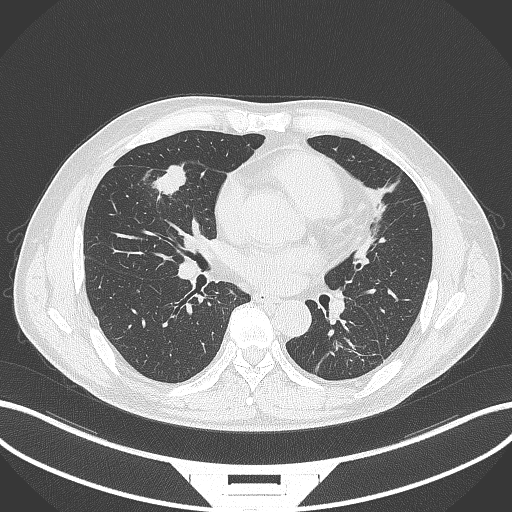
Chest CT, one axial slice. Slice 146 of 399 in the series (ordered by position). Reconstruction kernel B70f. 120 kVp. Lung window (W 1500 / L -600 HU). 1 mm slice thickness. 512 × 512 image matrix. Patient: male, 59 years. From the clinical record (not read from this slice): clinical TNM (as recorded): T2a N1 M0.
Annotated regions visible in this slice (bounding box drawn by a radiologist):
- lung tumour (recorded histology: adenocarcinoma): box from (x=150, y=160) to (x=187, y=200) px